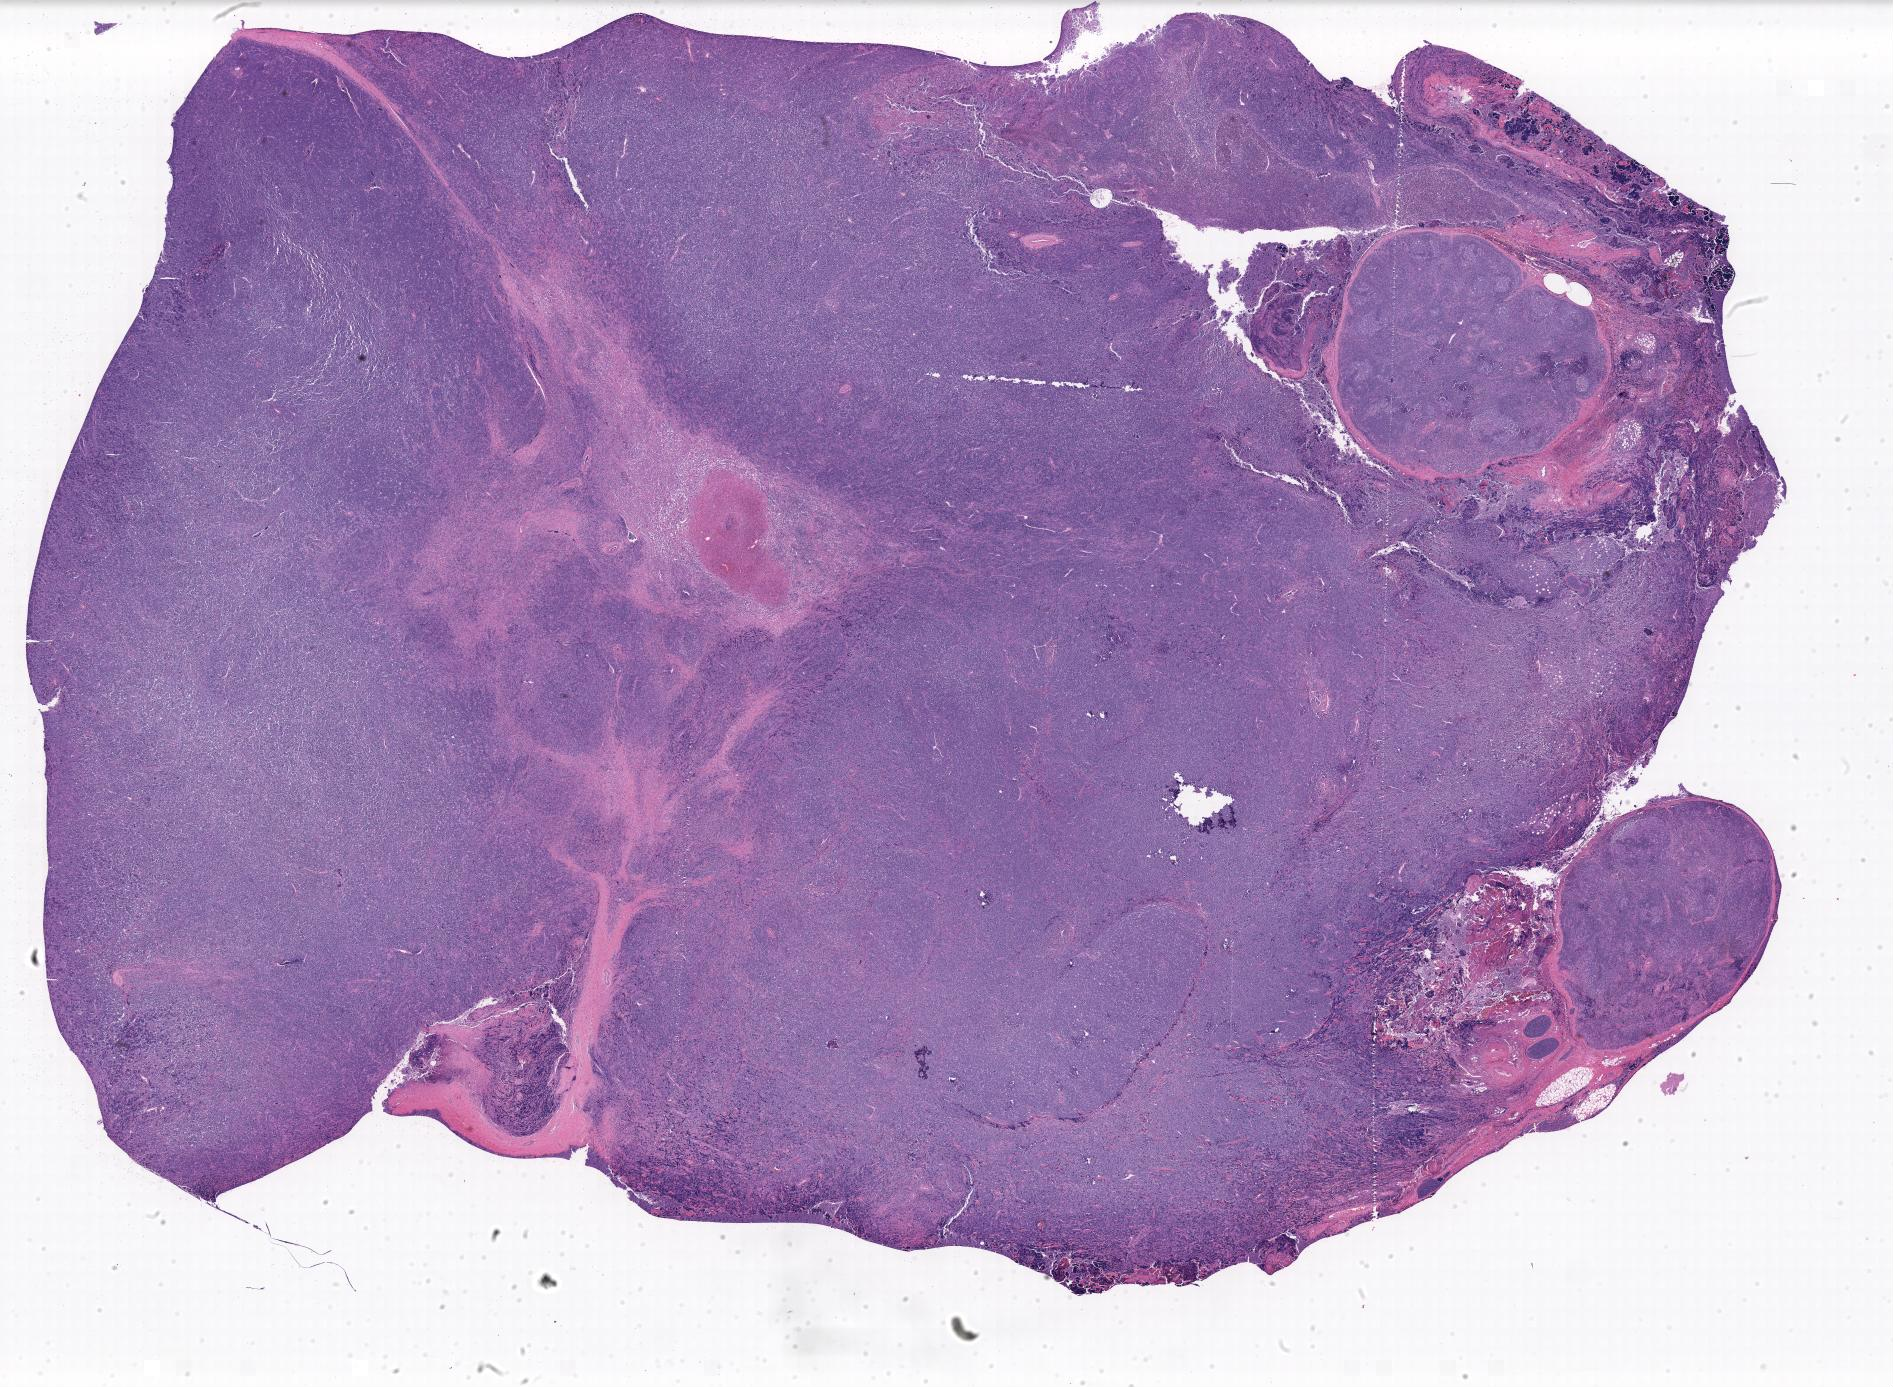
Digitized hematoxylin and eosin (H&E)-stained section — shown as a low-resolution overview of the whole scanned area. Tumor tissue. Anatomic site: lymph node of head and neck. Patient: male, age at initial diagnosis 3 years.
Diagnosis: Burkitt lymphoma, NOS.